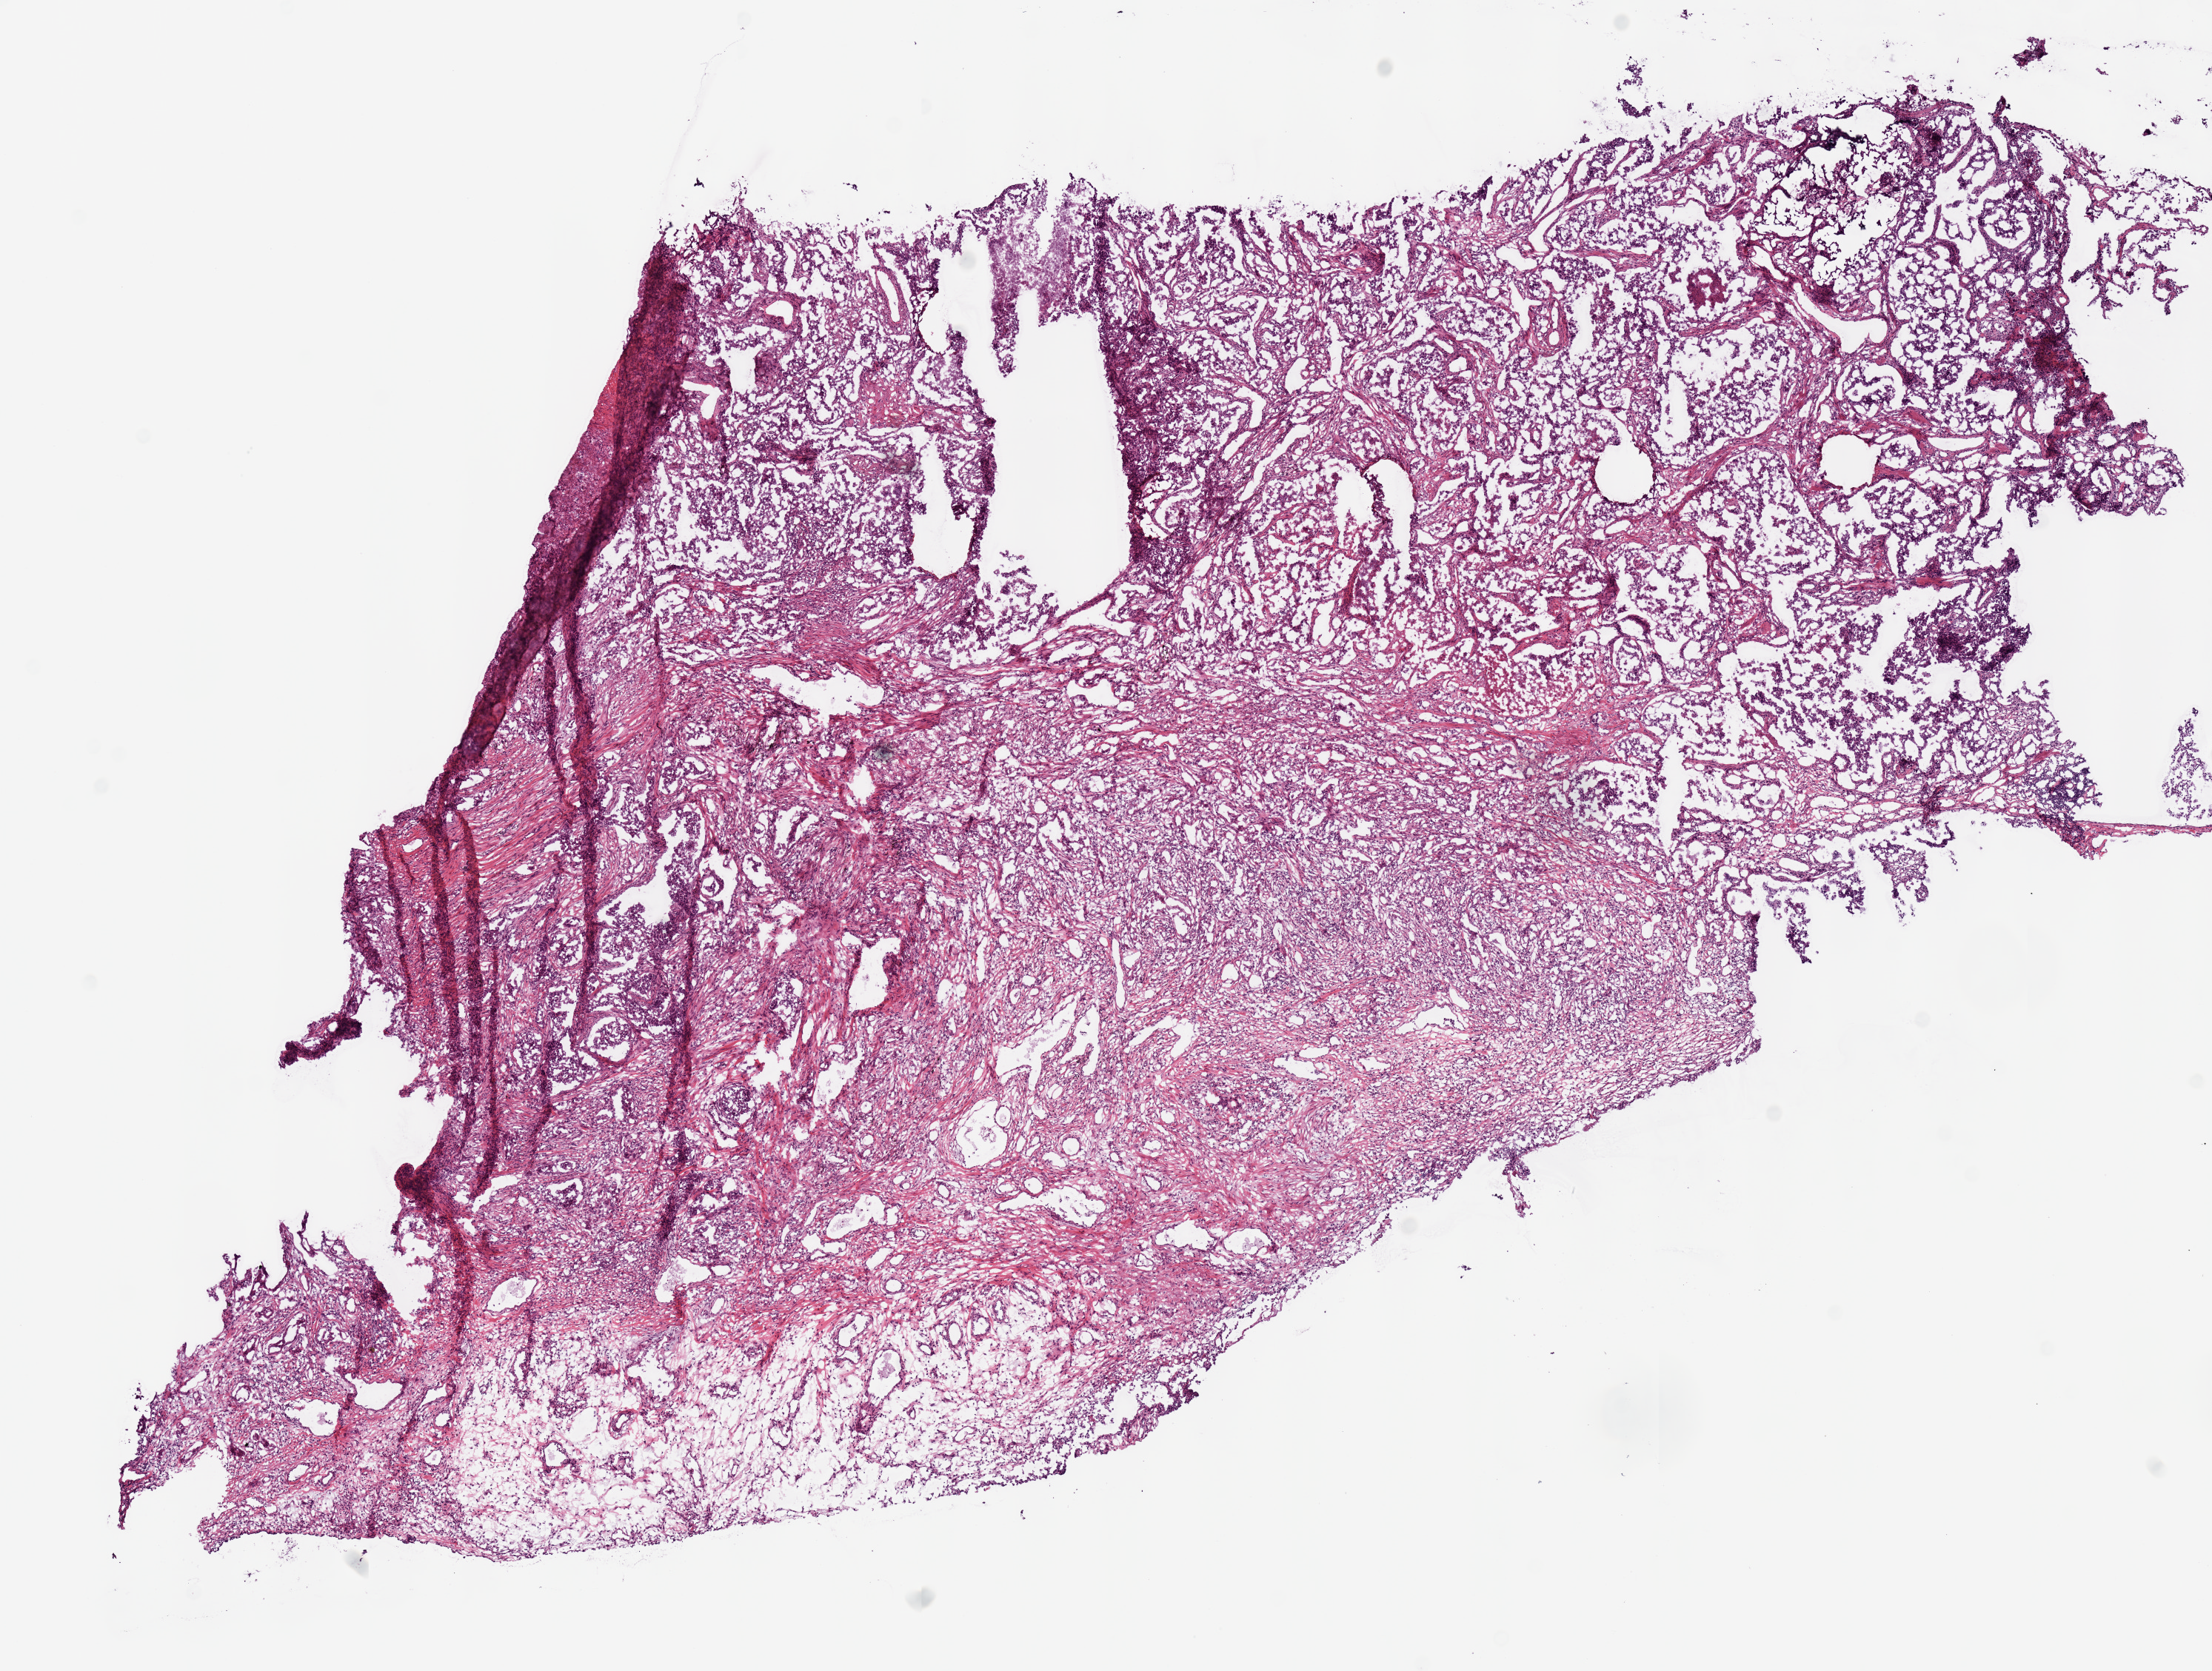
Whole-slide histology image, Hematoxylin and eosin (H&E) stained, whole scanned area (about 11.8 x 8.9 mm) shown as a low-resolution overview, frozen section, lung, primary tumour sample. Patient: female, age at initial diagnosis 68 years. Slide review estimates, as recorded: tumour cells 65%, tumour nuclei 70%, normal cells 0%, stromal cells 15%, necrosis 20%.
* pathologic diagnosis: Adenocarcinoma, NOS (upper lobe, lung)
* TNM: T1 N2 MX
* AJCC pathologic stage: IIIA (6th edition)
* laterality: right